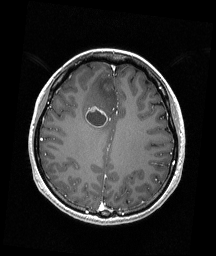
Brain MRI from a brain-tumour surgery series, one axial slice. Position 67 of 192 along the scan axis. T1-weighted post-contrast. 216 × 256 image matrix, field of view 211 × 250 mm. From the clinical record (not read from this slice): histopathology: Astrocytoma; WHO grade: 4; IDH mutation: yes.
Annotated regions visible in this slice (expert manual segmentation):
- tumour: bounding box (x1, y1, x2, y2) in pixels: (85, 106, 108, 127)